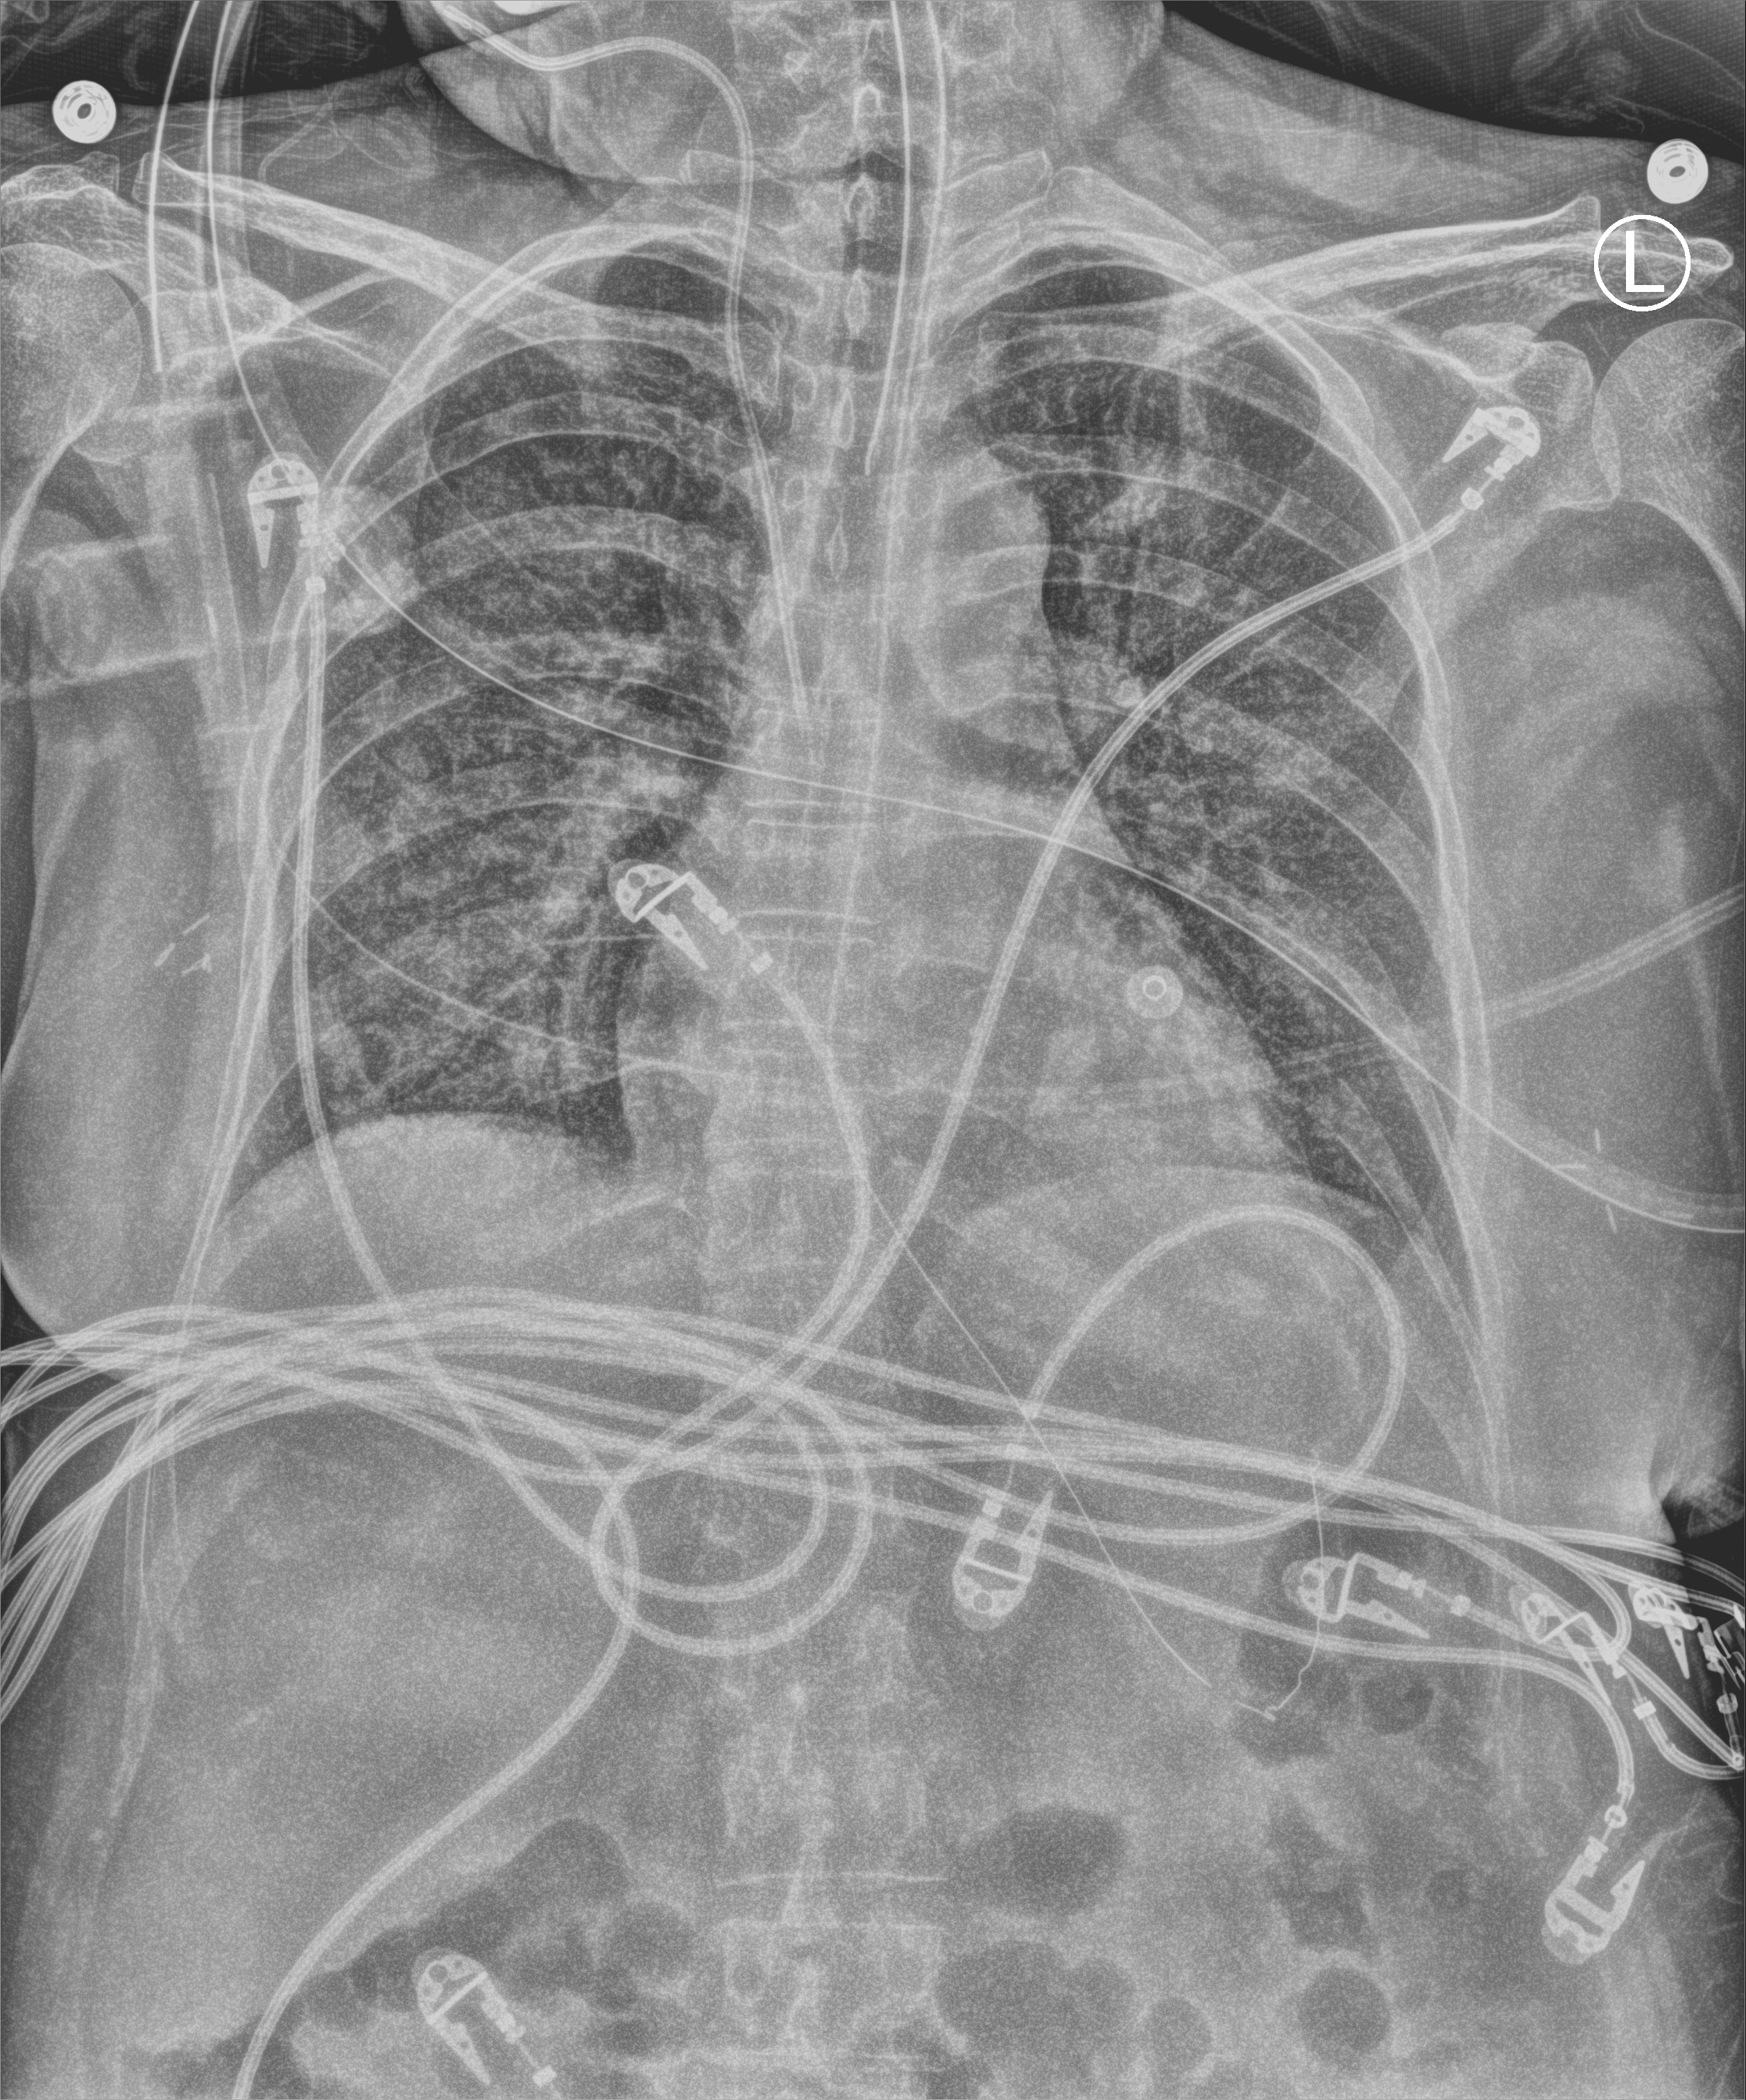
Chest X-ray (portable), anteroposterior (AP) projection. Female patient hospitalised with COVID-19, age 18–59 years.
Admission-level facts for this patient (not findings on this image; timing relative to this image not recorded):
- hypertension (admission record): no
- mechanically ventilated during this hospital stay: yes
- admitted to intensive care during this hospital stay: no